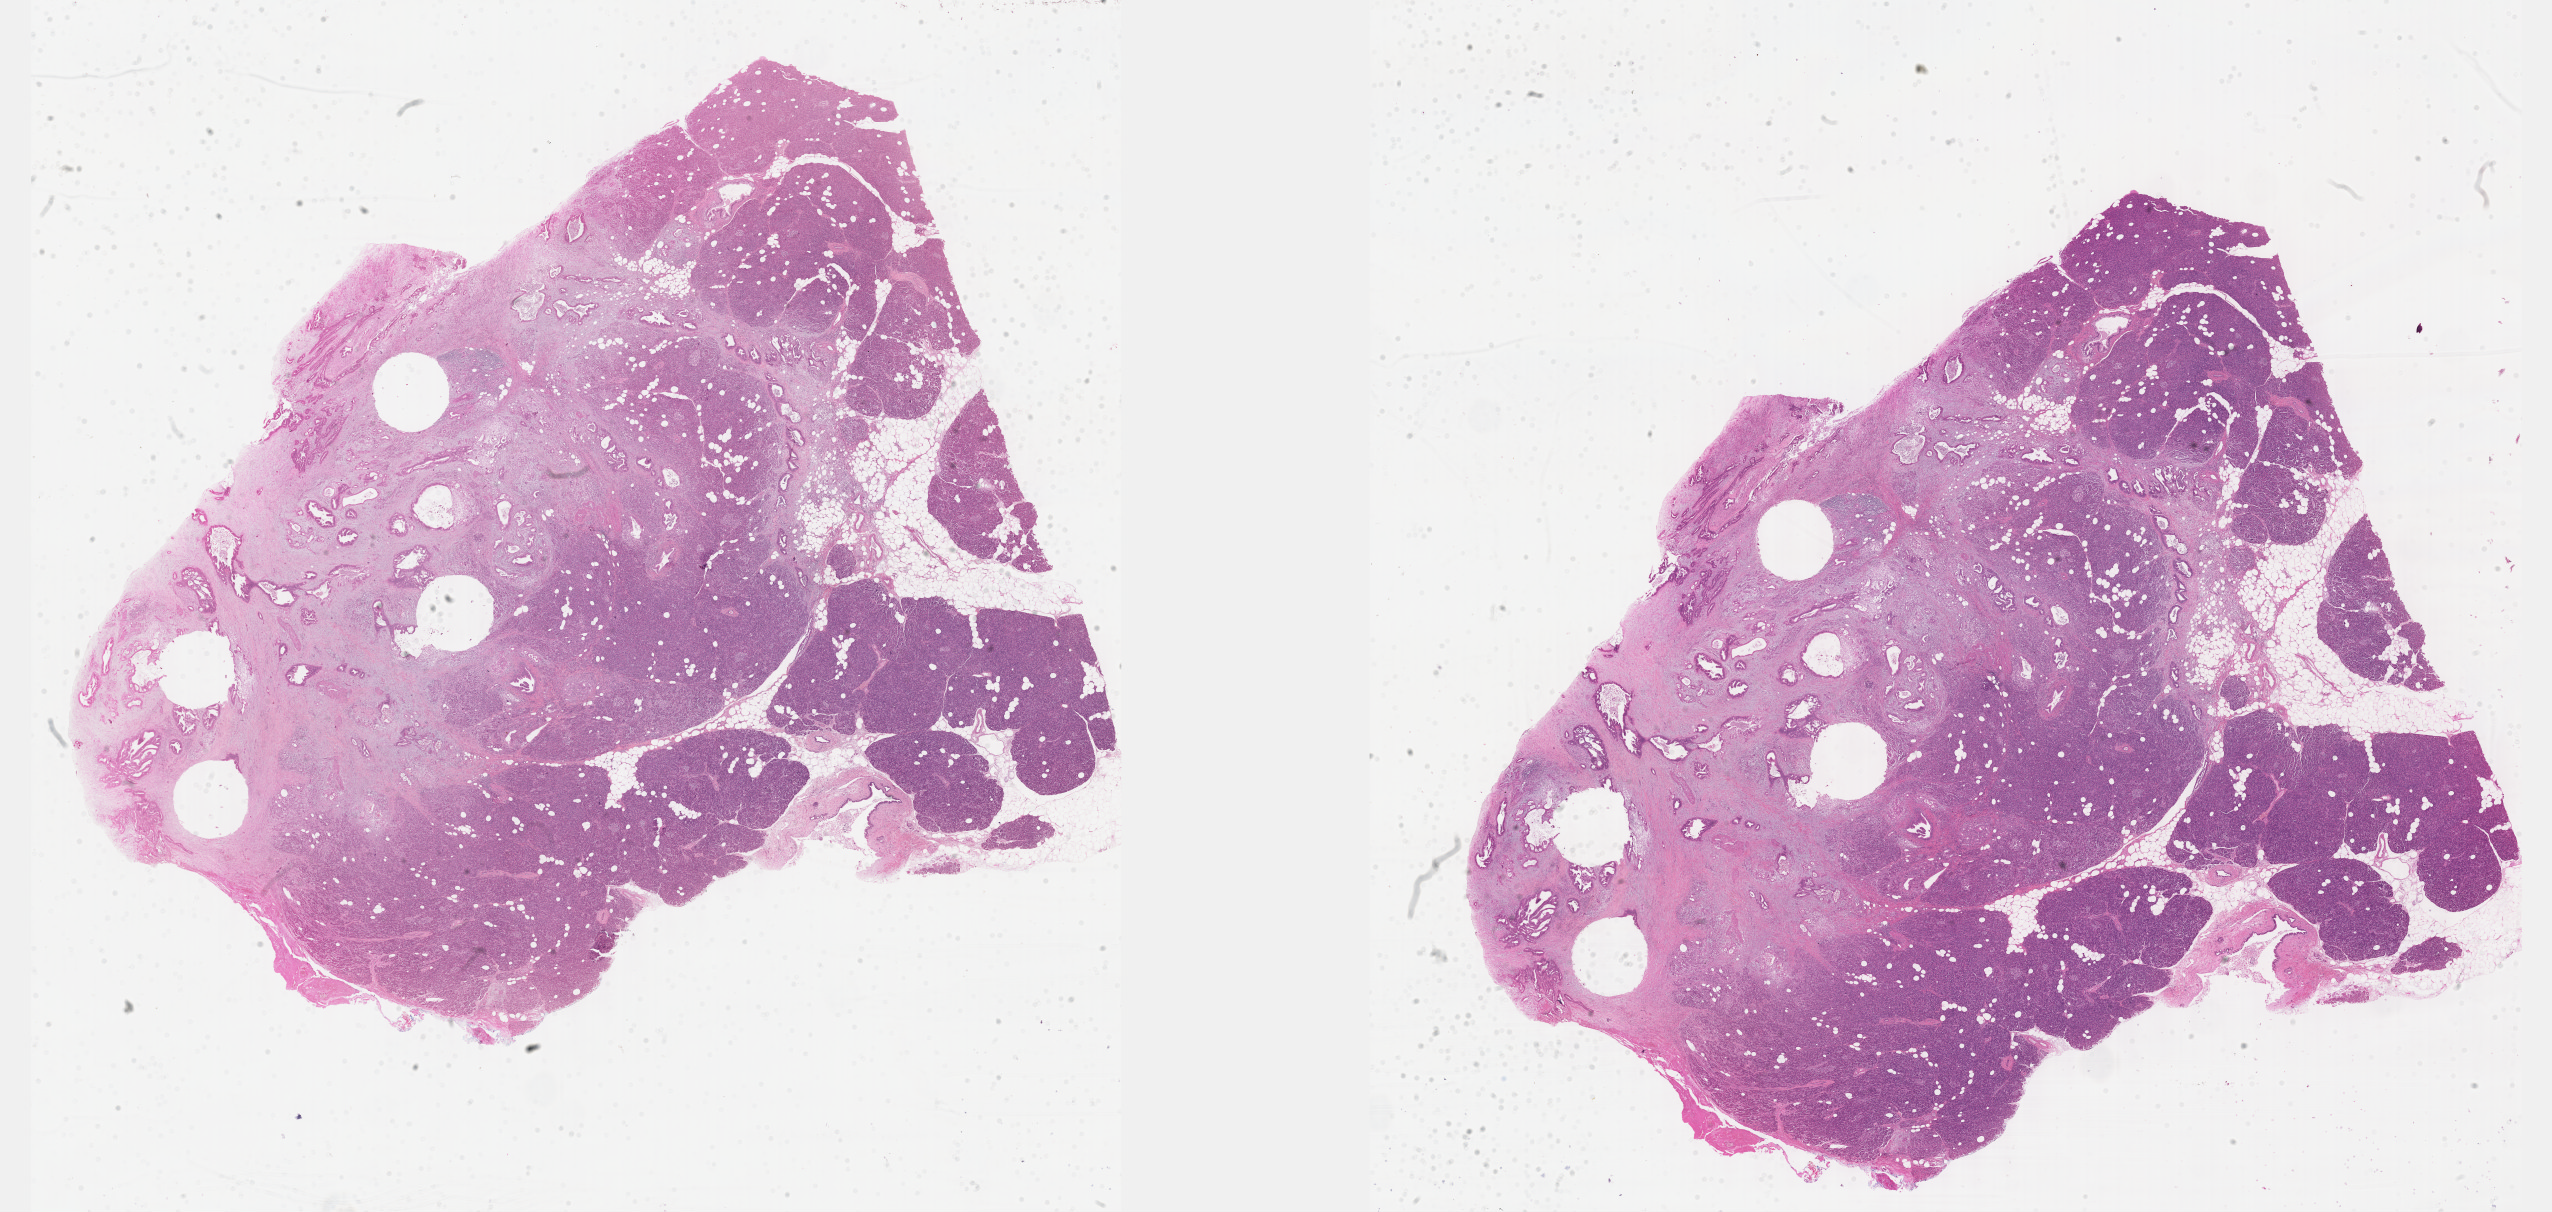
Digitized H&E-stained tissue section (whole slide) — whole scanned area (about 41.2 x 19.6 mm) shown as a low-resolution overview. Formalin-fixed paraffin-embedded (FFPE) diagnostic section. Sample: primary tumour, pancreas. Male, age 64 years at initial diagnosis. Histologic grade: G2 (moderately differentiated).
Pathologic diagnosis: Infiltrating duct carcinoma, NOS. AJCC pathologic stage: IIB (7th edition).